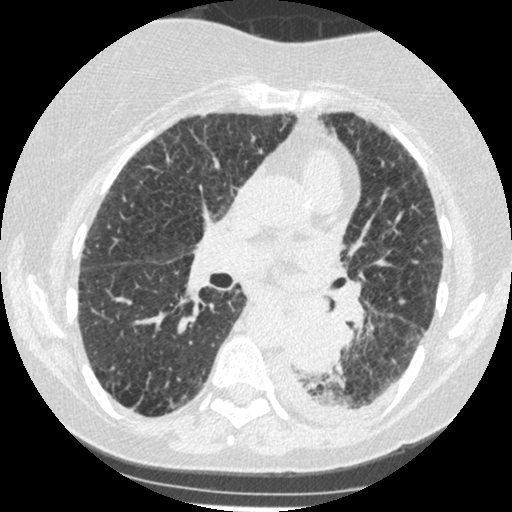
Low-dose screening chest CT, one axial slice; slice 135 of 341 in the series (ordered by position); reconstruction kernel STANDARD; 120 kVp; lung window (W 1500 / L -600 HU); 512 × 512 image matrix.
Annotated regions visible in this slice (expert manual segmentation):
- lesion 1 (tumor, lower lobe of left lung): bounding box <285,309,341,374> (left, top, right, bottom; pixels)